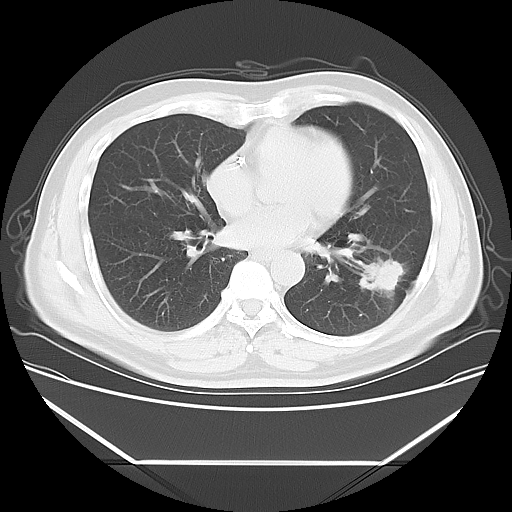
Chest CT, one axial slice. Position 26 of 57 along the scan axis. Reconstruction kernel LUNG. 120 kVp. Lung window (W 1500 / L -600 HU). 5 mm slice thickness. 512 × 512 image matrix. Male patient, age 53 years. Case-level facts recorded for this patient, not image findings: clinical TNM (as recorded): T1c N0 M0; histopathological grade: G2-3.
Structures marked on this image (bounding box drawn by a radiologist):
- lung tumour (recorded histology: adenocarcinoma): bounding box (x1, y1, x2, y2) in pixels: (354, 247, 414, 309)